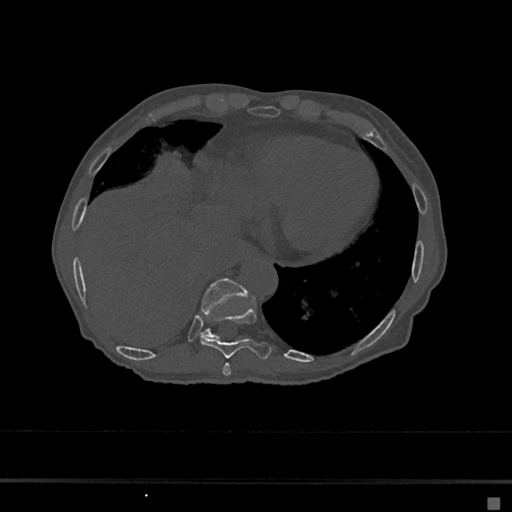
CT including the spine, one axial slice; slice 261 of 797 in the series (ordered by position); 120 kVp; bone window (W 1800 / L 400 HU); 0.5 mm slice thickness; 512 × 512 image matrix, field of view 360 × 360 mm. Female patient, age 68 years. From the clinical record (not read from this slice): primary cancer: renal.
Annotated regions visible in this slice (semi-automatic segmentation, software-assisted and operator-edited):
- T10 vertebra: bounding box (x1, y1, x2, y2) in pixels: (200, 278, 248, 339)
- T8 vertebra: (222, 363, 231, 376)
- T9 vertebra: (200, 306, 272, 360)